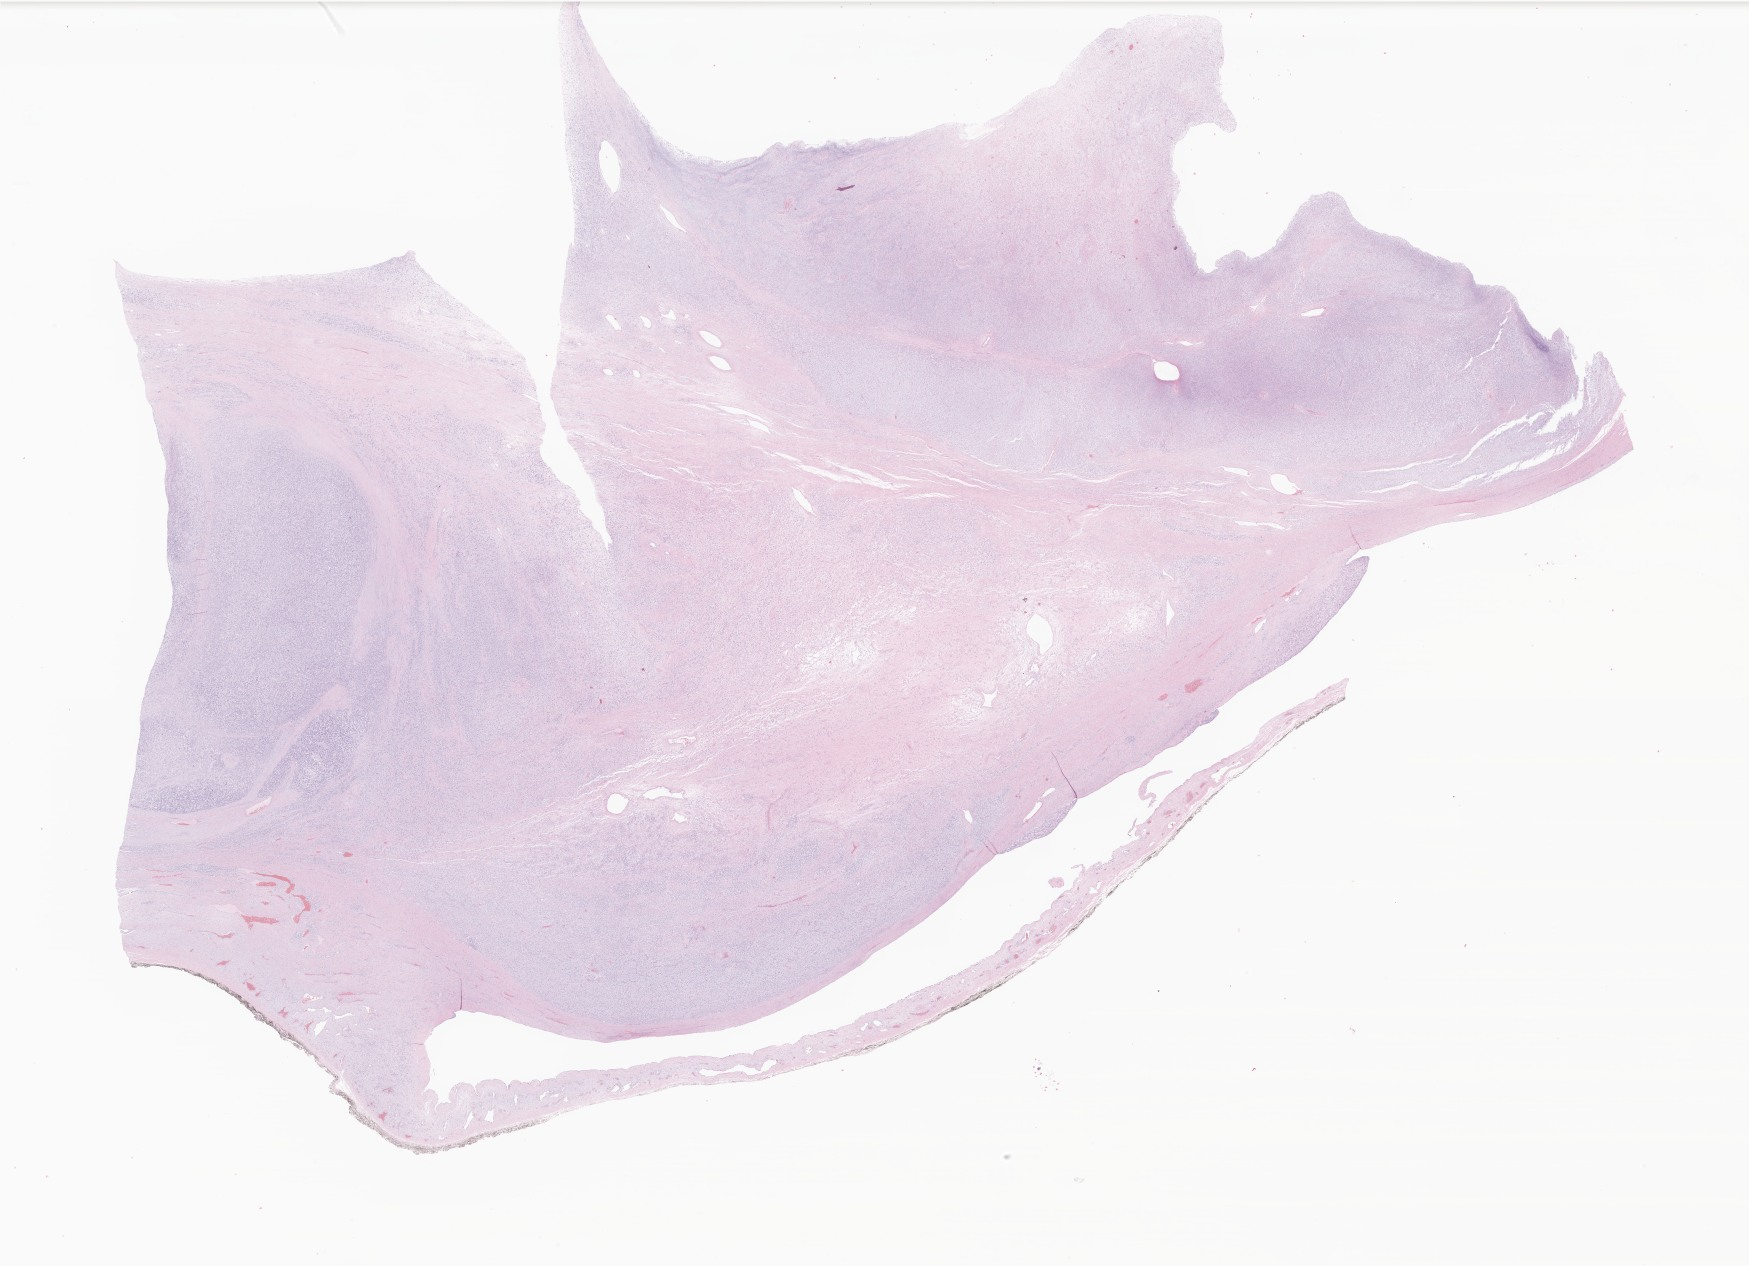
Haematoxylin and eosin whole-slide image of tumor tissue from the testis, low-resolution overview of the scanned area, about 29.5 x 21.4 mm, formalin-fixed paraffin-embedded section. Male patient, age 174 months (14 years 6 months).
• diagnosis (ICD-O-3 morphology term): Rhabdomyosarcoma, NOS